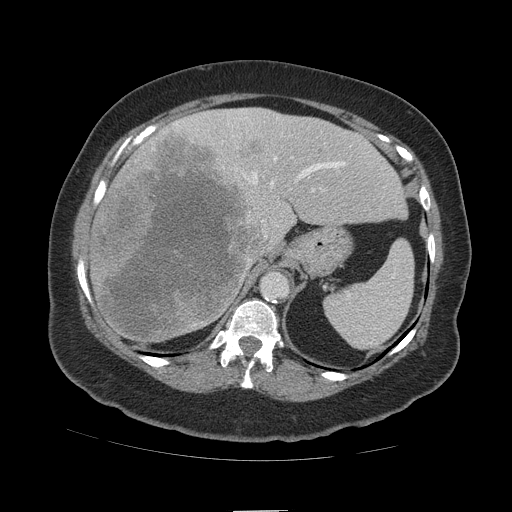
Contrast-enhanced abdominal CT (liver protocol), one axial slice; position 77 of 109 along the scan axis; reconstruction kernel STANDARD; 140 kVp; soft-tissue window (W 400 / L 40 HU); 512 × 512 image matrix, field of view 420 × 420 mm. Case-level facts recorded for this patient, not image findings: diagnosis: hepatocellular carcinoma (patient treated with transarterial chemoembolisation; whether this scan precedes or follows treatment is not stated here); TNM stage (as recorded): Stage-IVB; Child-Pugh class: A; tumour nodularity: multinodular.
Outlined on this slice (semi-automatic segmentation, software-assisted and operator-edited):
- liver parenchyma outside the tumour (the mass and vessels are separate outlines, so this box may not span the whole liver): bounding box [x1, y1, x2, y2] px = [88, 108, 406, 341]
- mass: [90, 131, 273, 347]
- liver vessels: [174, 110, 346, 192]